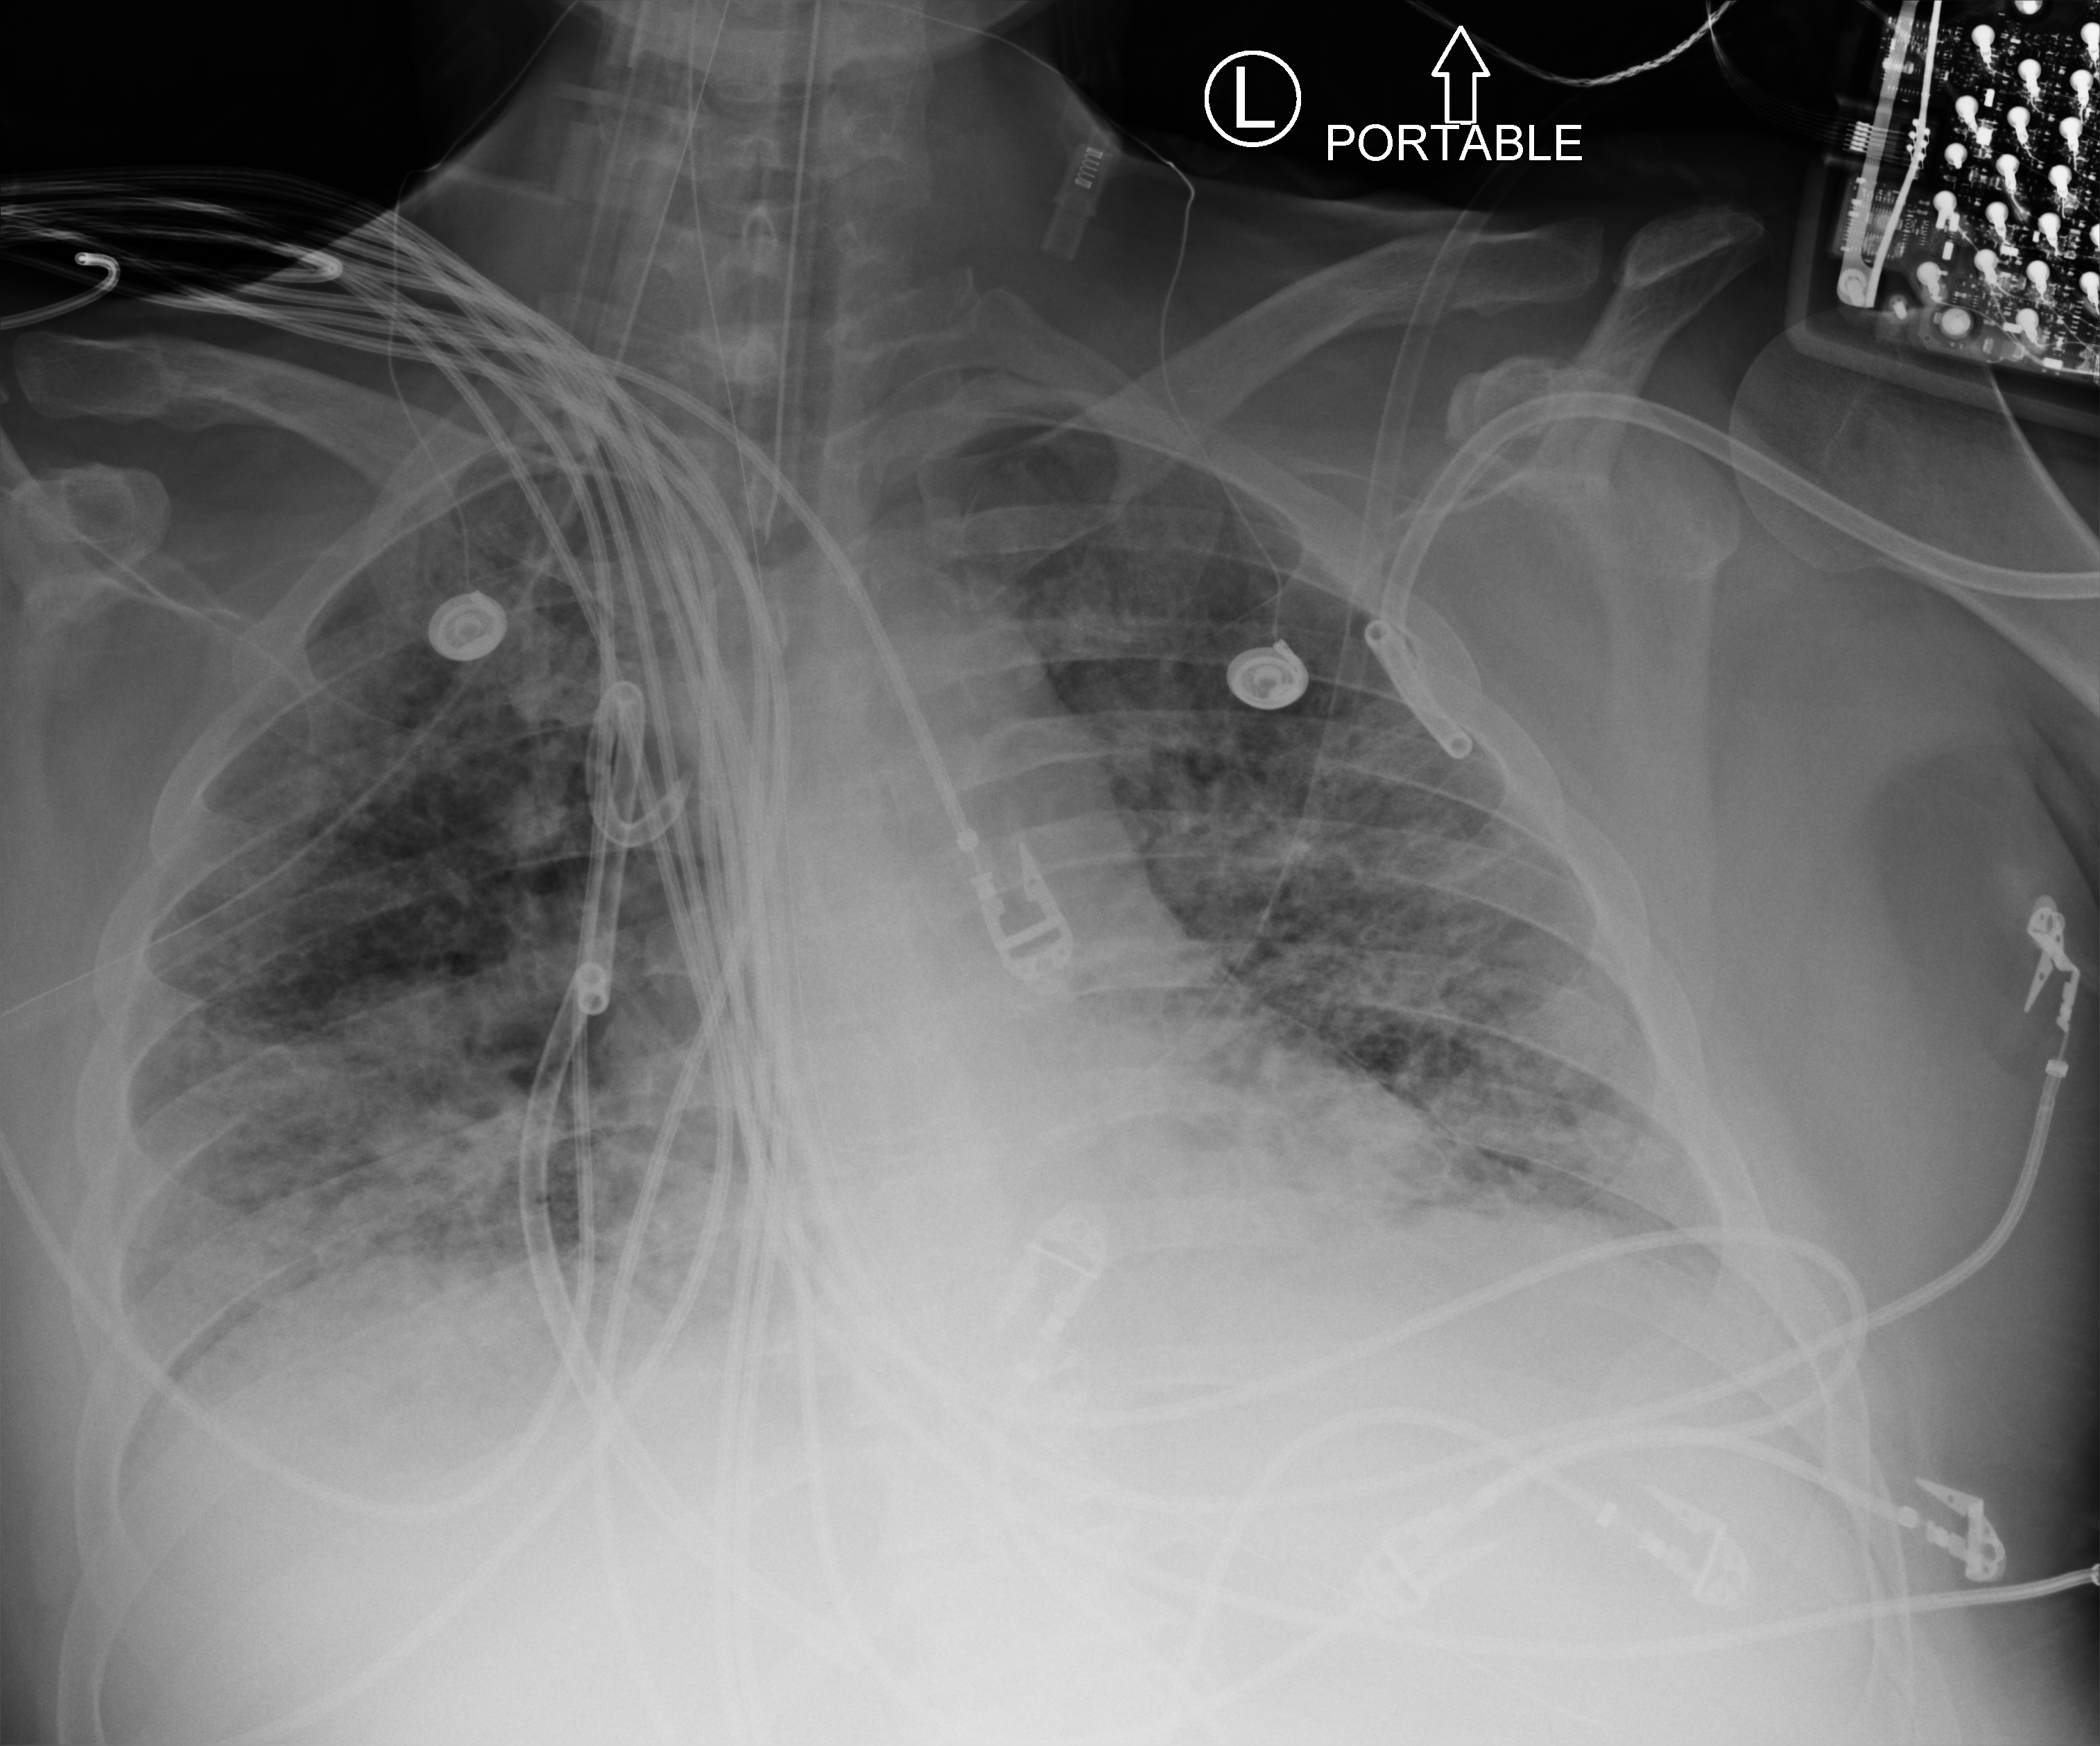
Portable chest radiograph, anteroposterior (AP) projection. Patient hospitalised with COVID-19, aged 18–59 years.
Hospital-stay facts (about this admission, not read from this image; timing relative to this image not recorded): admitted to intensive care during this hospital stay: yes.